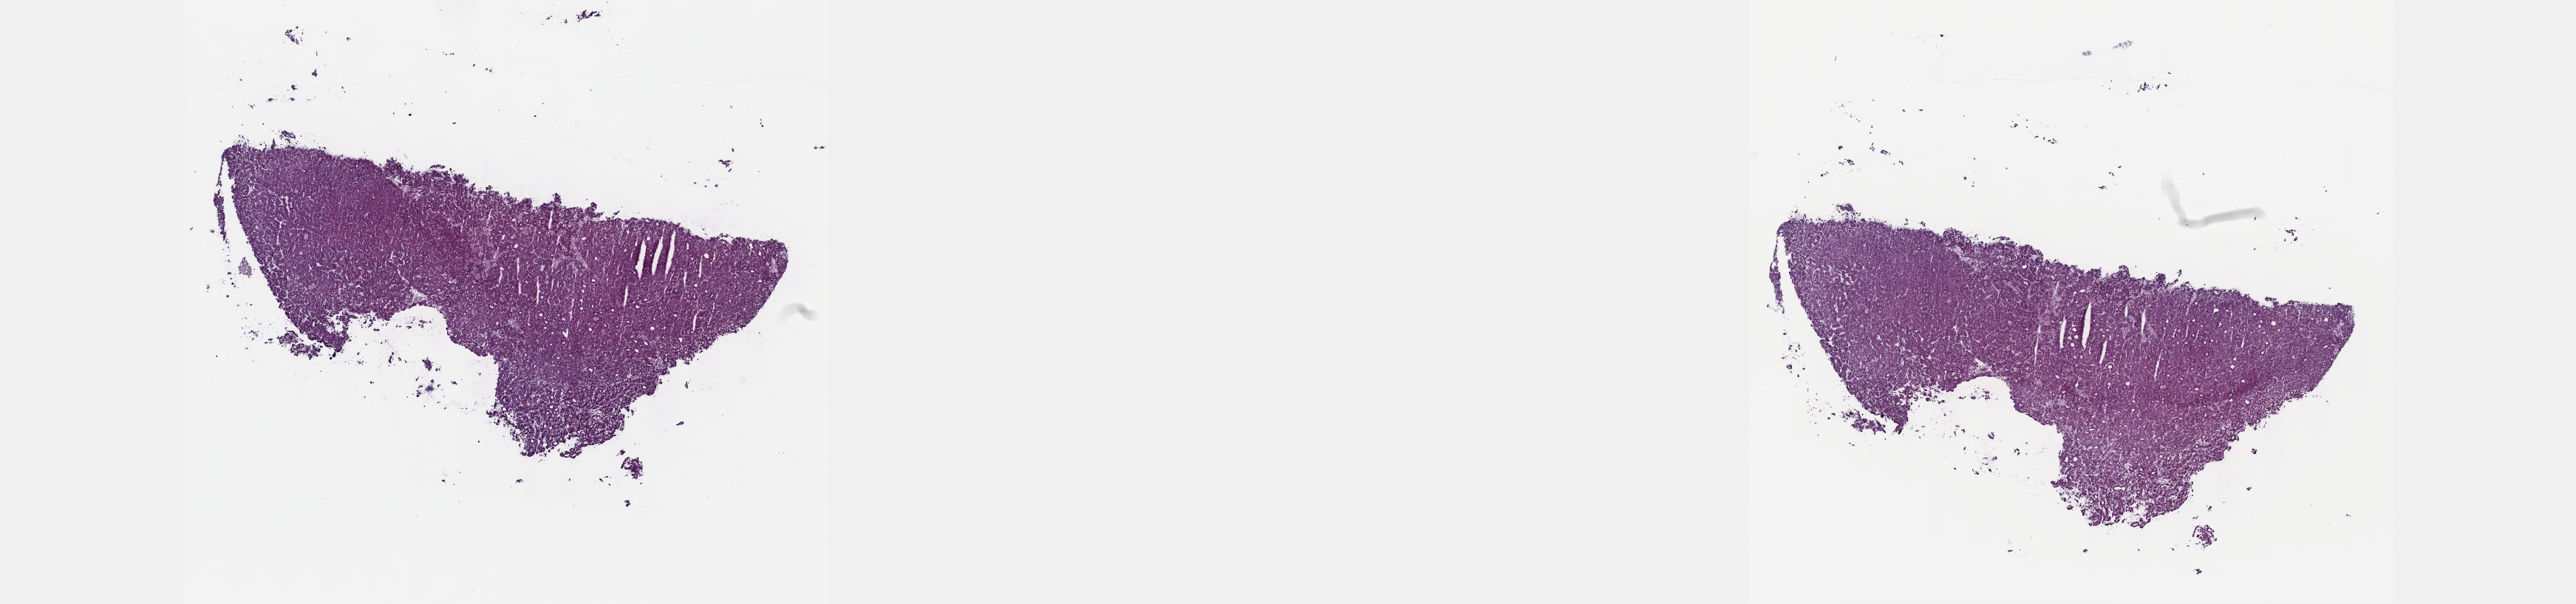
H&E whole-slide image — low-resolution overview of the scanned area, about 28.2 x 6.6 mm; frozen section from the top of the tissue portion; primary tumour sample from the liver. Patient: female, age at initial diagnosis 64 years. Histologic grade: G1 (well differentiated). Composition of this section per pathologist review: tumour cells 100%, tumour nuclei 85%, normal cells 0%, stromal cells 0%, necrosis 0%. Infiltration values recorded for this section: lymphocyte infiltration 0%, monocyte infiltration 0%, neutrophil infiltration 0%.
• pathologic diagnosis: Hepatocellular carcinoma, NOS